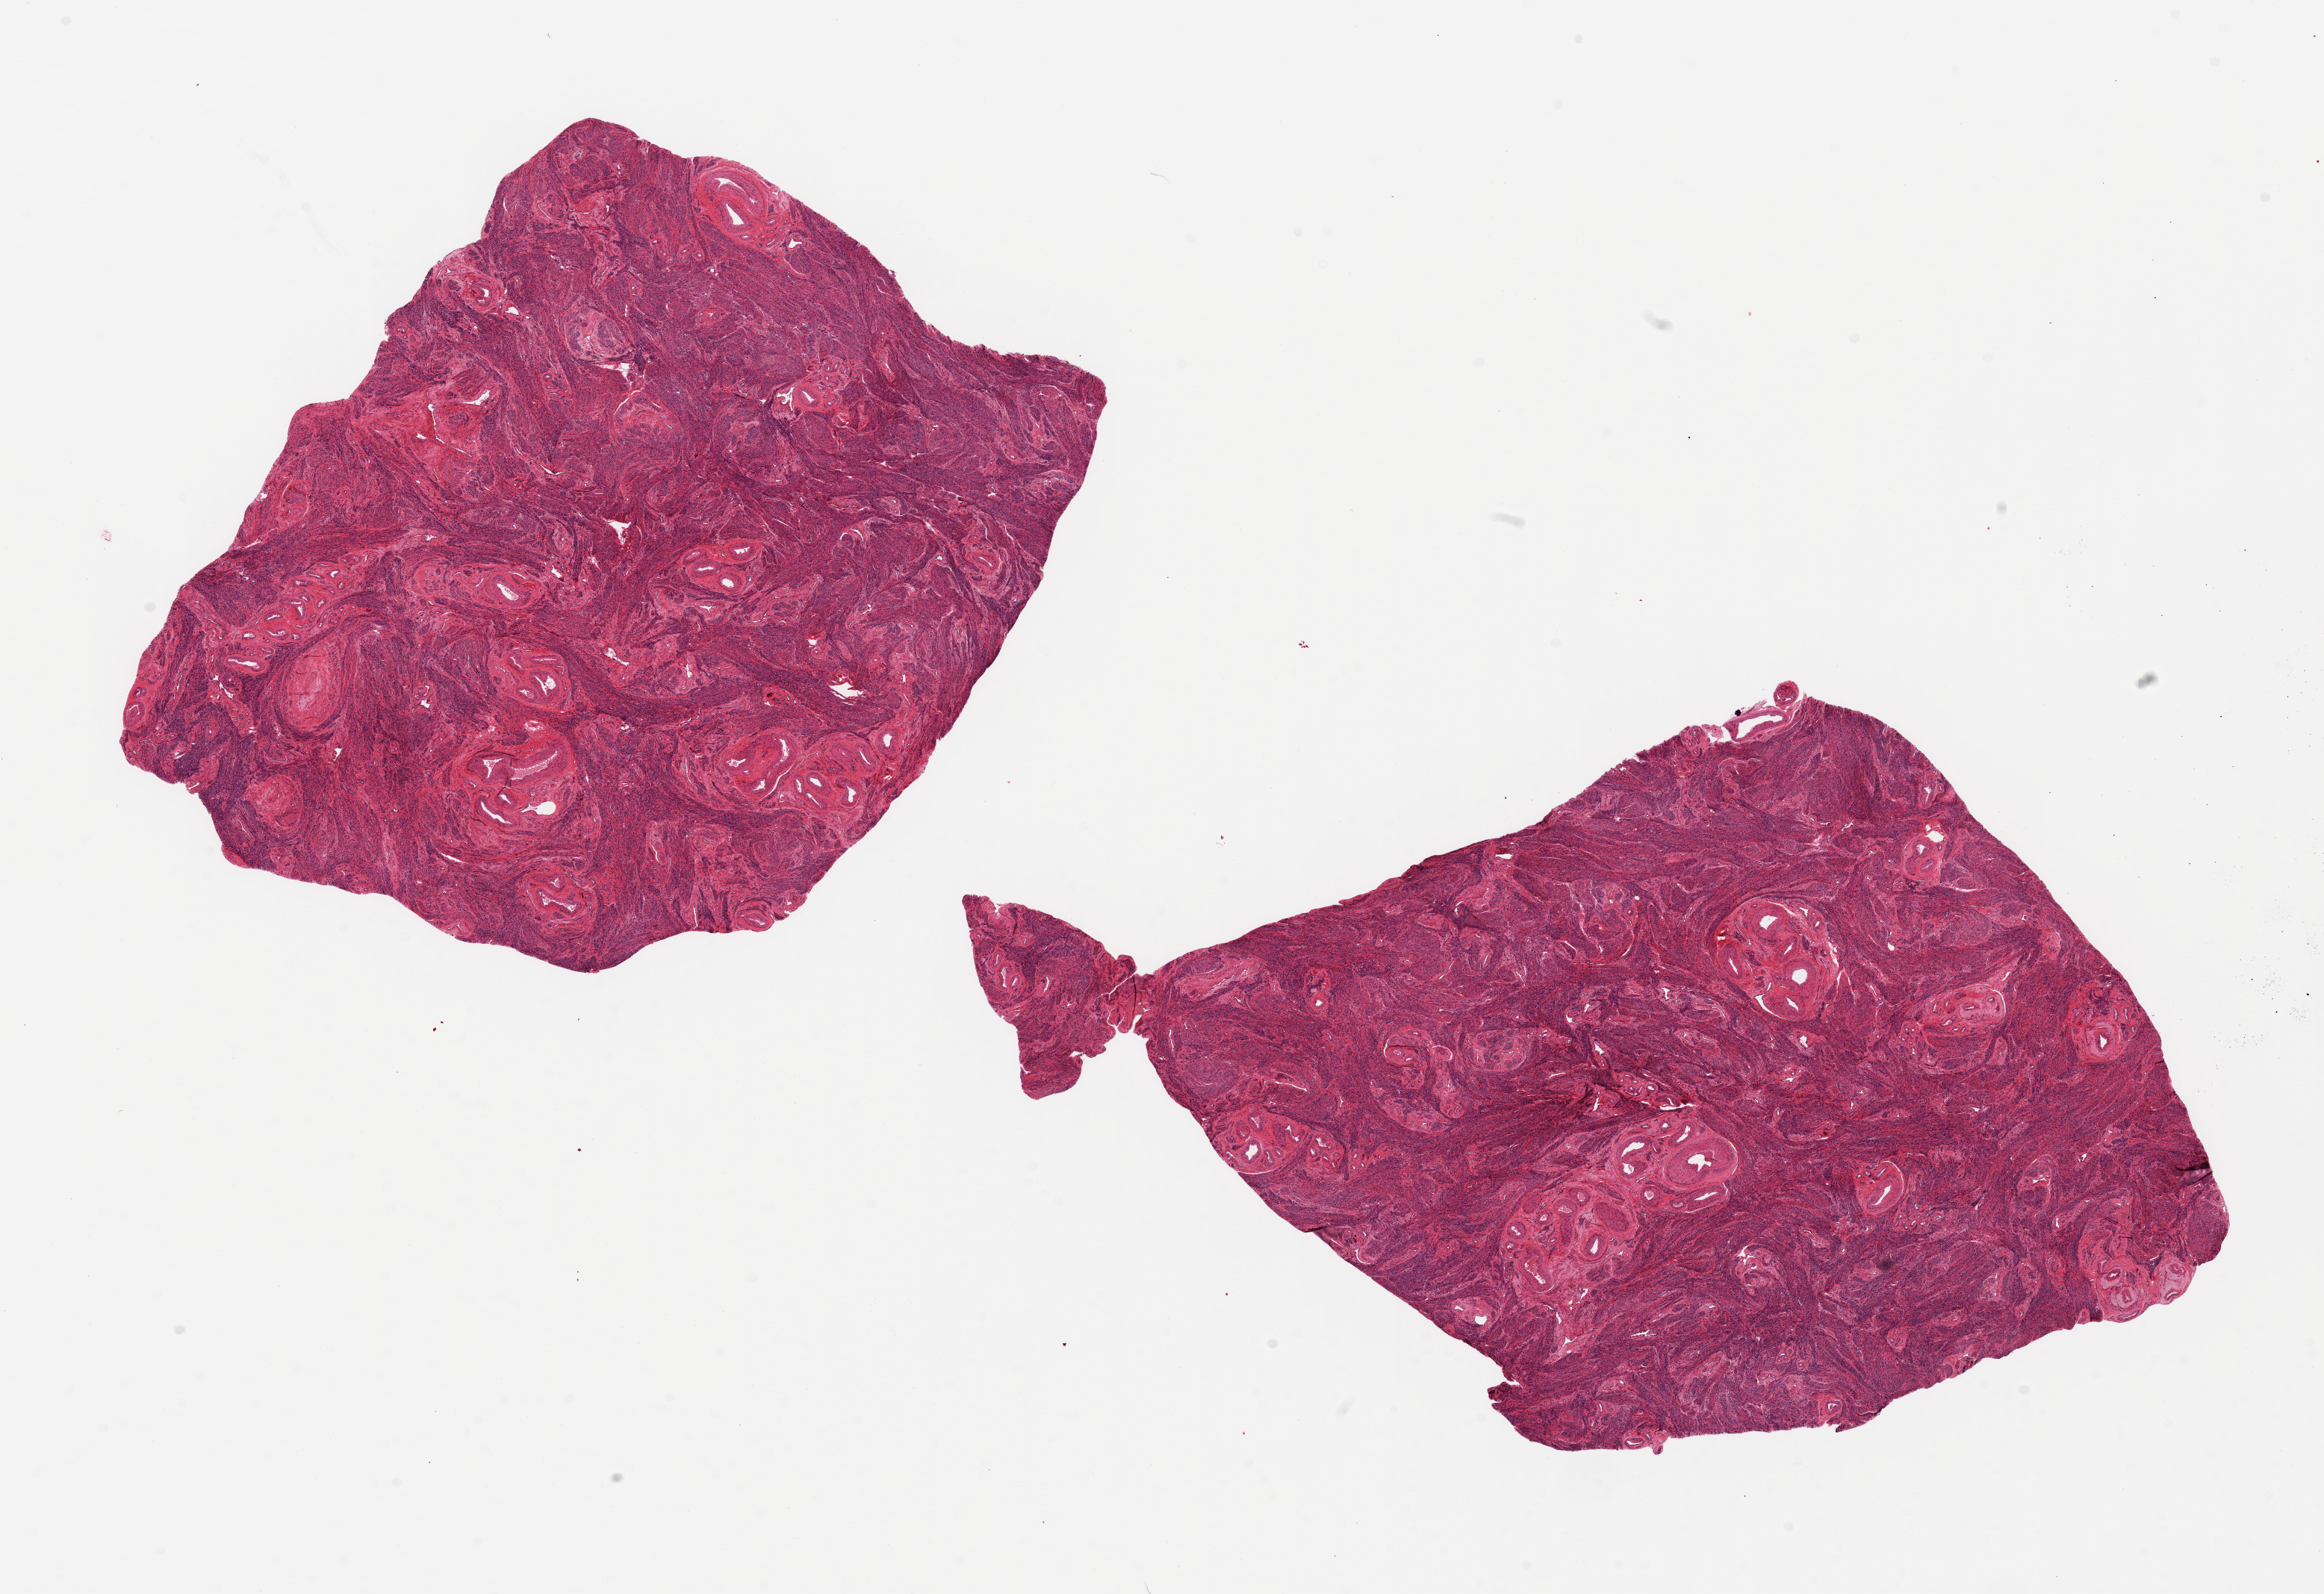
Digitized hematoxylin and eosin (H&E)-stained section, low-resolution overview of the scanned area, about 24.6 x 16.9 mm (slide scanned at 20x); PAXgene-fixed paraffin-embedded (PFPE) section; target tissue: uterus; tissue donor sample. Donor sex: female.
Review note (as recorded): 2 pieces ~8x8mm. All muscularis, no glands/stroma noted.